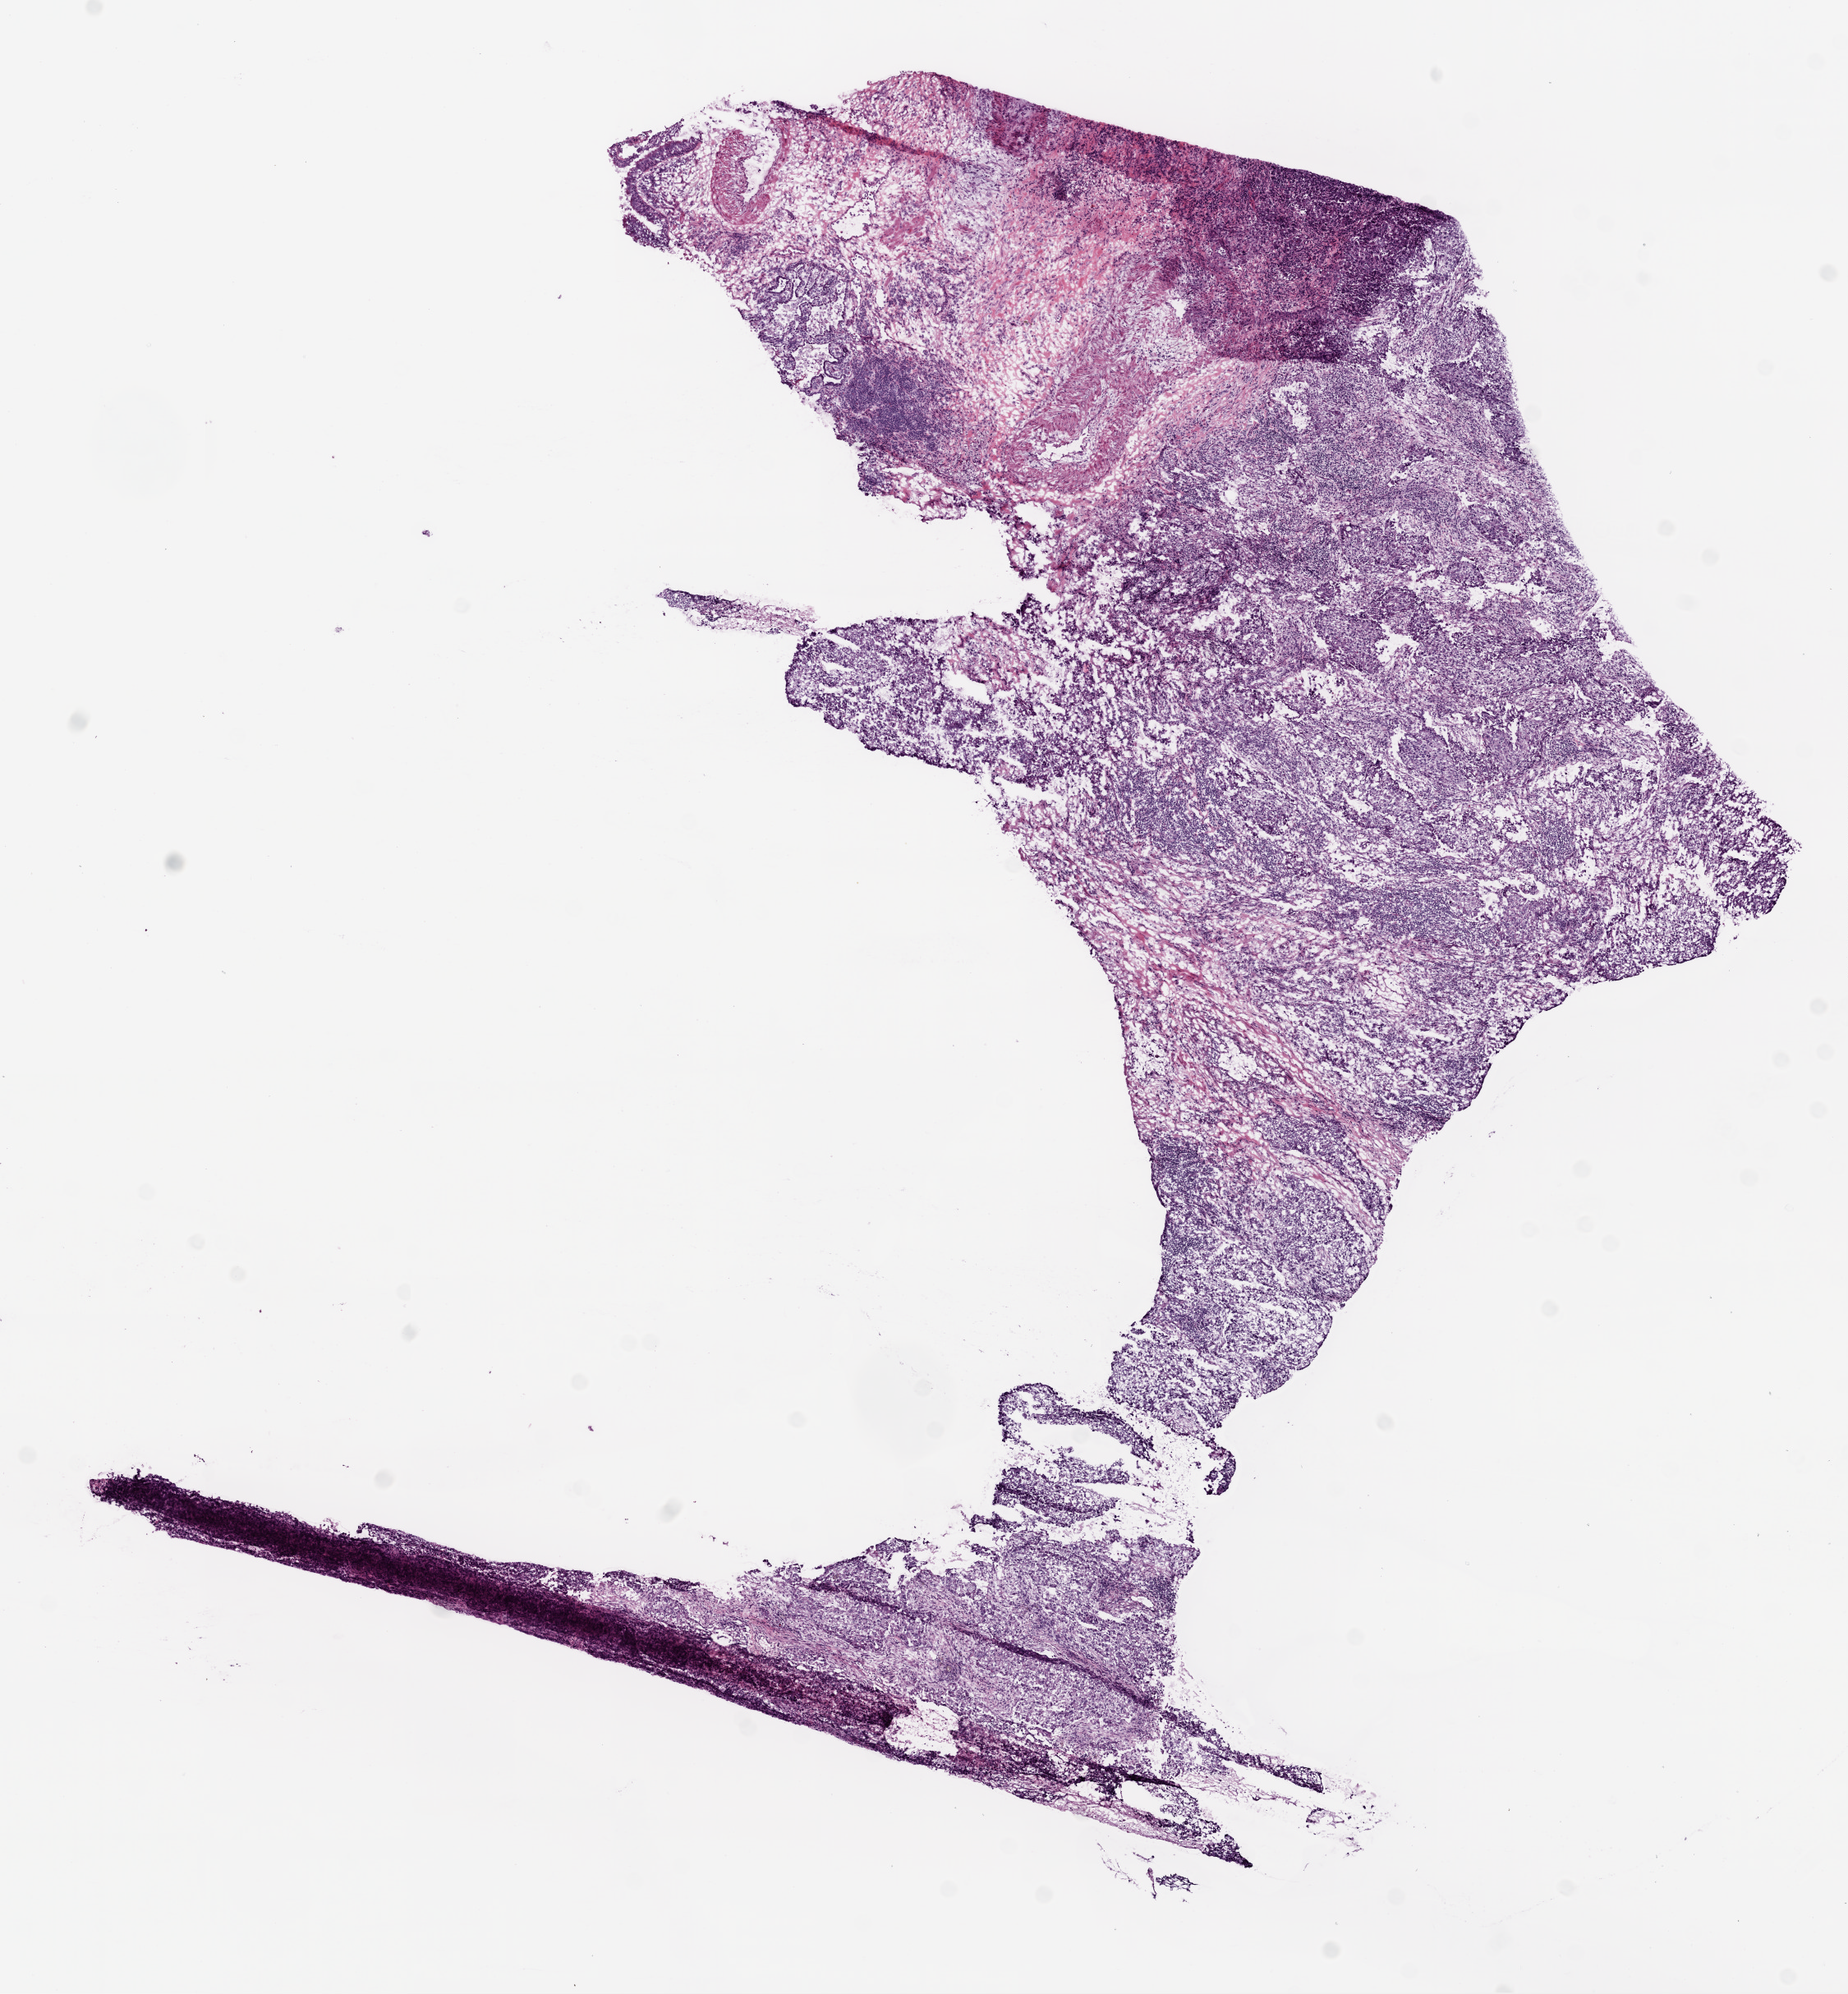
Digitized H&E-stained tissue section (whole slide), whole scanned area (about 9.0 x 9.7 mm, acquisition: 20x scan) shown as a low-resolution overview; frozen section from the bottom of the tissue portion; sample: primary tumour, lung. Female patient; age at initial diagnosis 51 years. Pathologist review of this section (percent, as recorded): tumour cells 68%, tumour nuclei 60%, normal cells 20%, stromal cells 10%, necrosis 2%.
• TNM: T2 N0 M0
• AJCC pathologic stage: IB
• pathologic diagnosis: Adenocarcinoma with mixed subtypes